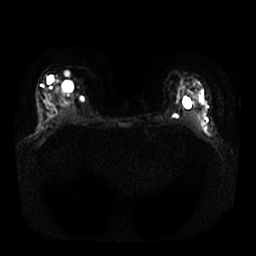
Breast MRI, one axial slice. Slice 17 of 25 in the series (ordered by position). Diffusion-weighted series; image 2 of 4 stored at this slice position (different b-values; order by instance number). 1.5 T. 4 mm slice thickness. 256 × 256 image matrix, field of view 340 × 340 mm. Female patient.
Outlined on this slice (outlined manually by an expert reader):
- tumour on diffusion-weighted imaging: bounding box (x1, y1, x2, y2) in pixels: (196, 89, 208, 120)